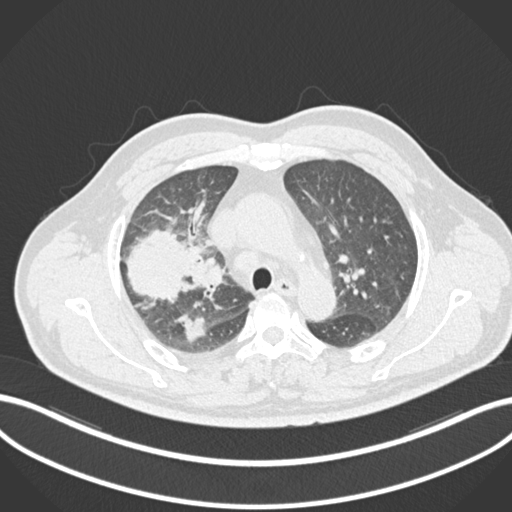
Chest CT, one axial slice; position 662 of 852 along the scan axis; 120 kVp; lung window (W 1500 / L -600 HU); 1 mm slice thickness; 512 × 512 image matrix. Patient: male, 55 years. From the clinical record (not read from this slice): clinical TNM (as recorded): T3 N2 M1.
Outlined on this slice (bounding box drawn by a radiologist):
- lung tumour (recorded histology: adenocarcinoma): bounding box (x1, y1, x2, y2) in pixels: (121, 223, 199, 305)